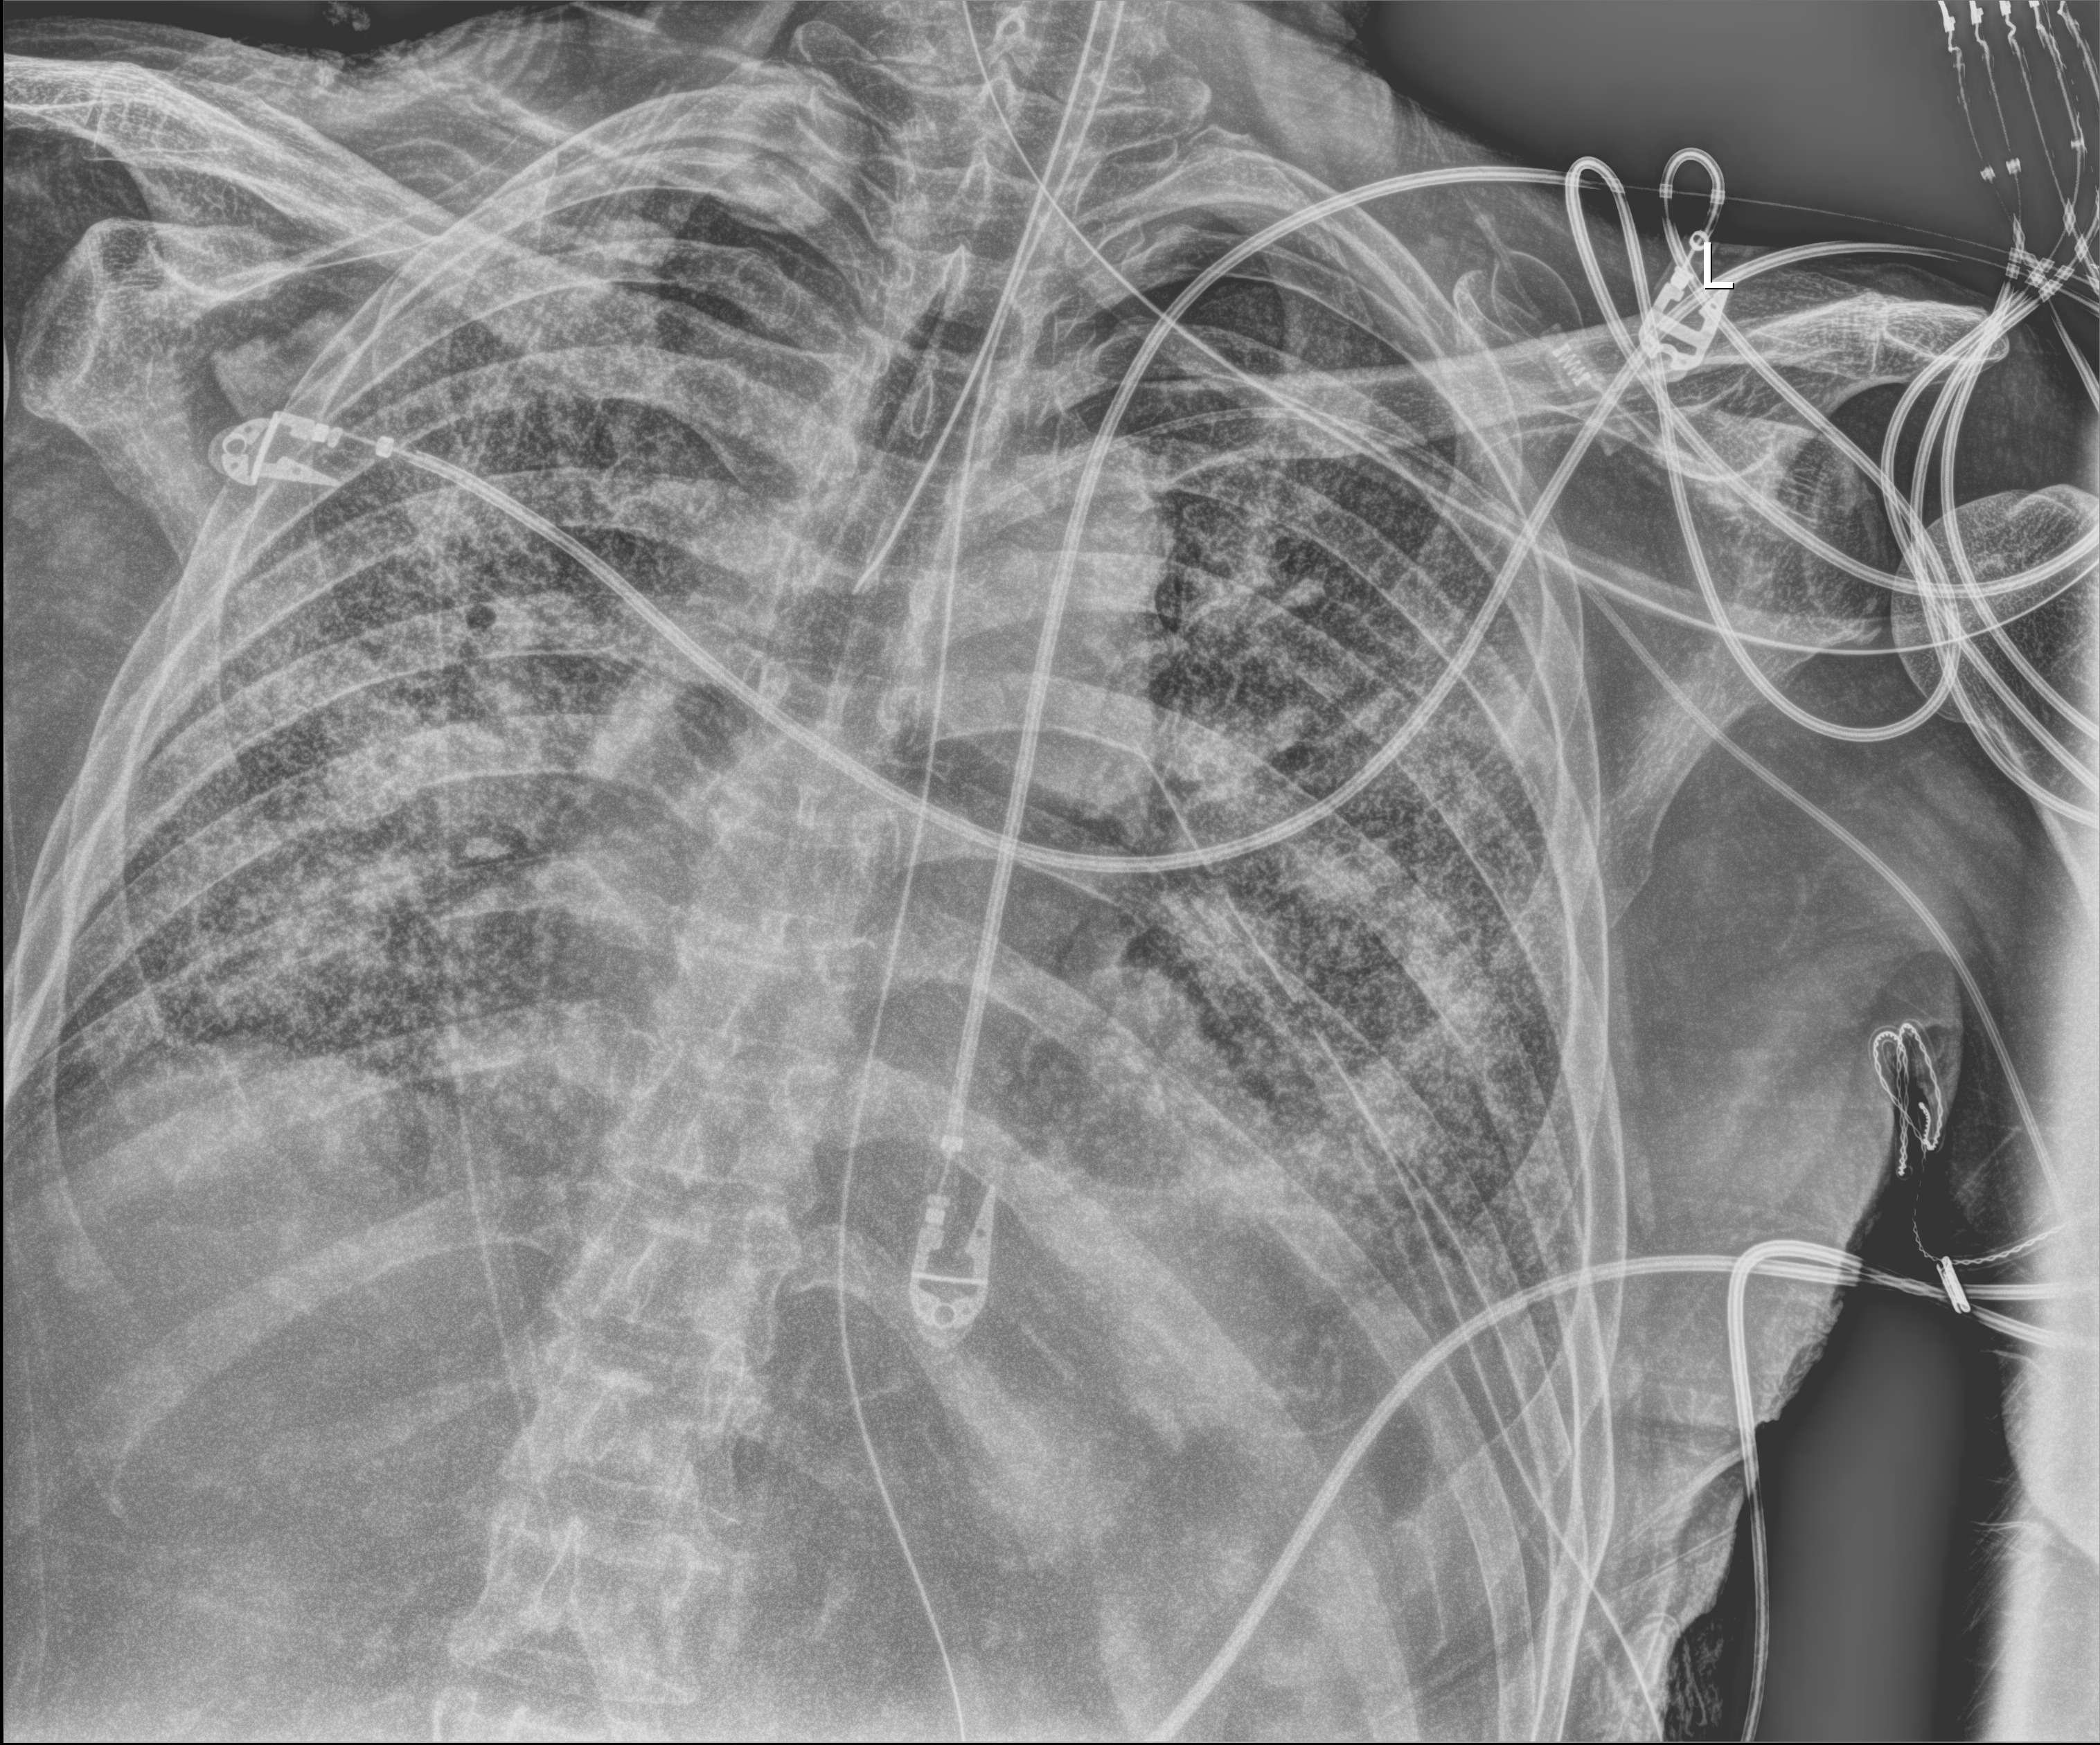
Chest X-ray; anteroposterior (AP) projection. Patient hospitalised with COVID-19; male, aged 60–74 years.
Admission-level facts for this patient (not findings on this image; timing relative to this image not recorded):
- mechanically ventilated during this hospital stay: yes
- admitted to intensive care during this hospital stay: yes
- length of hospital stay: 54 days